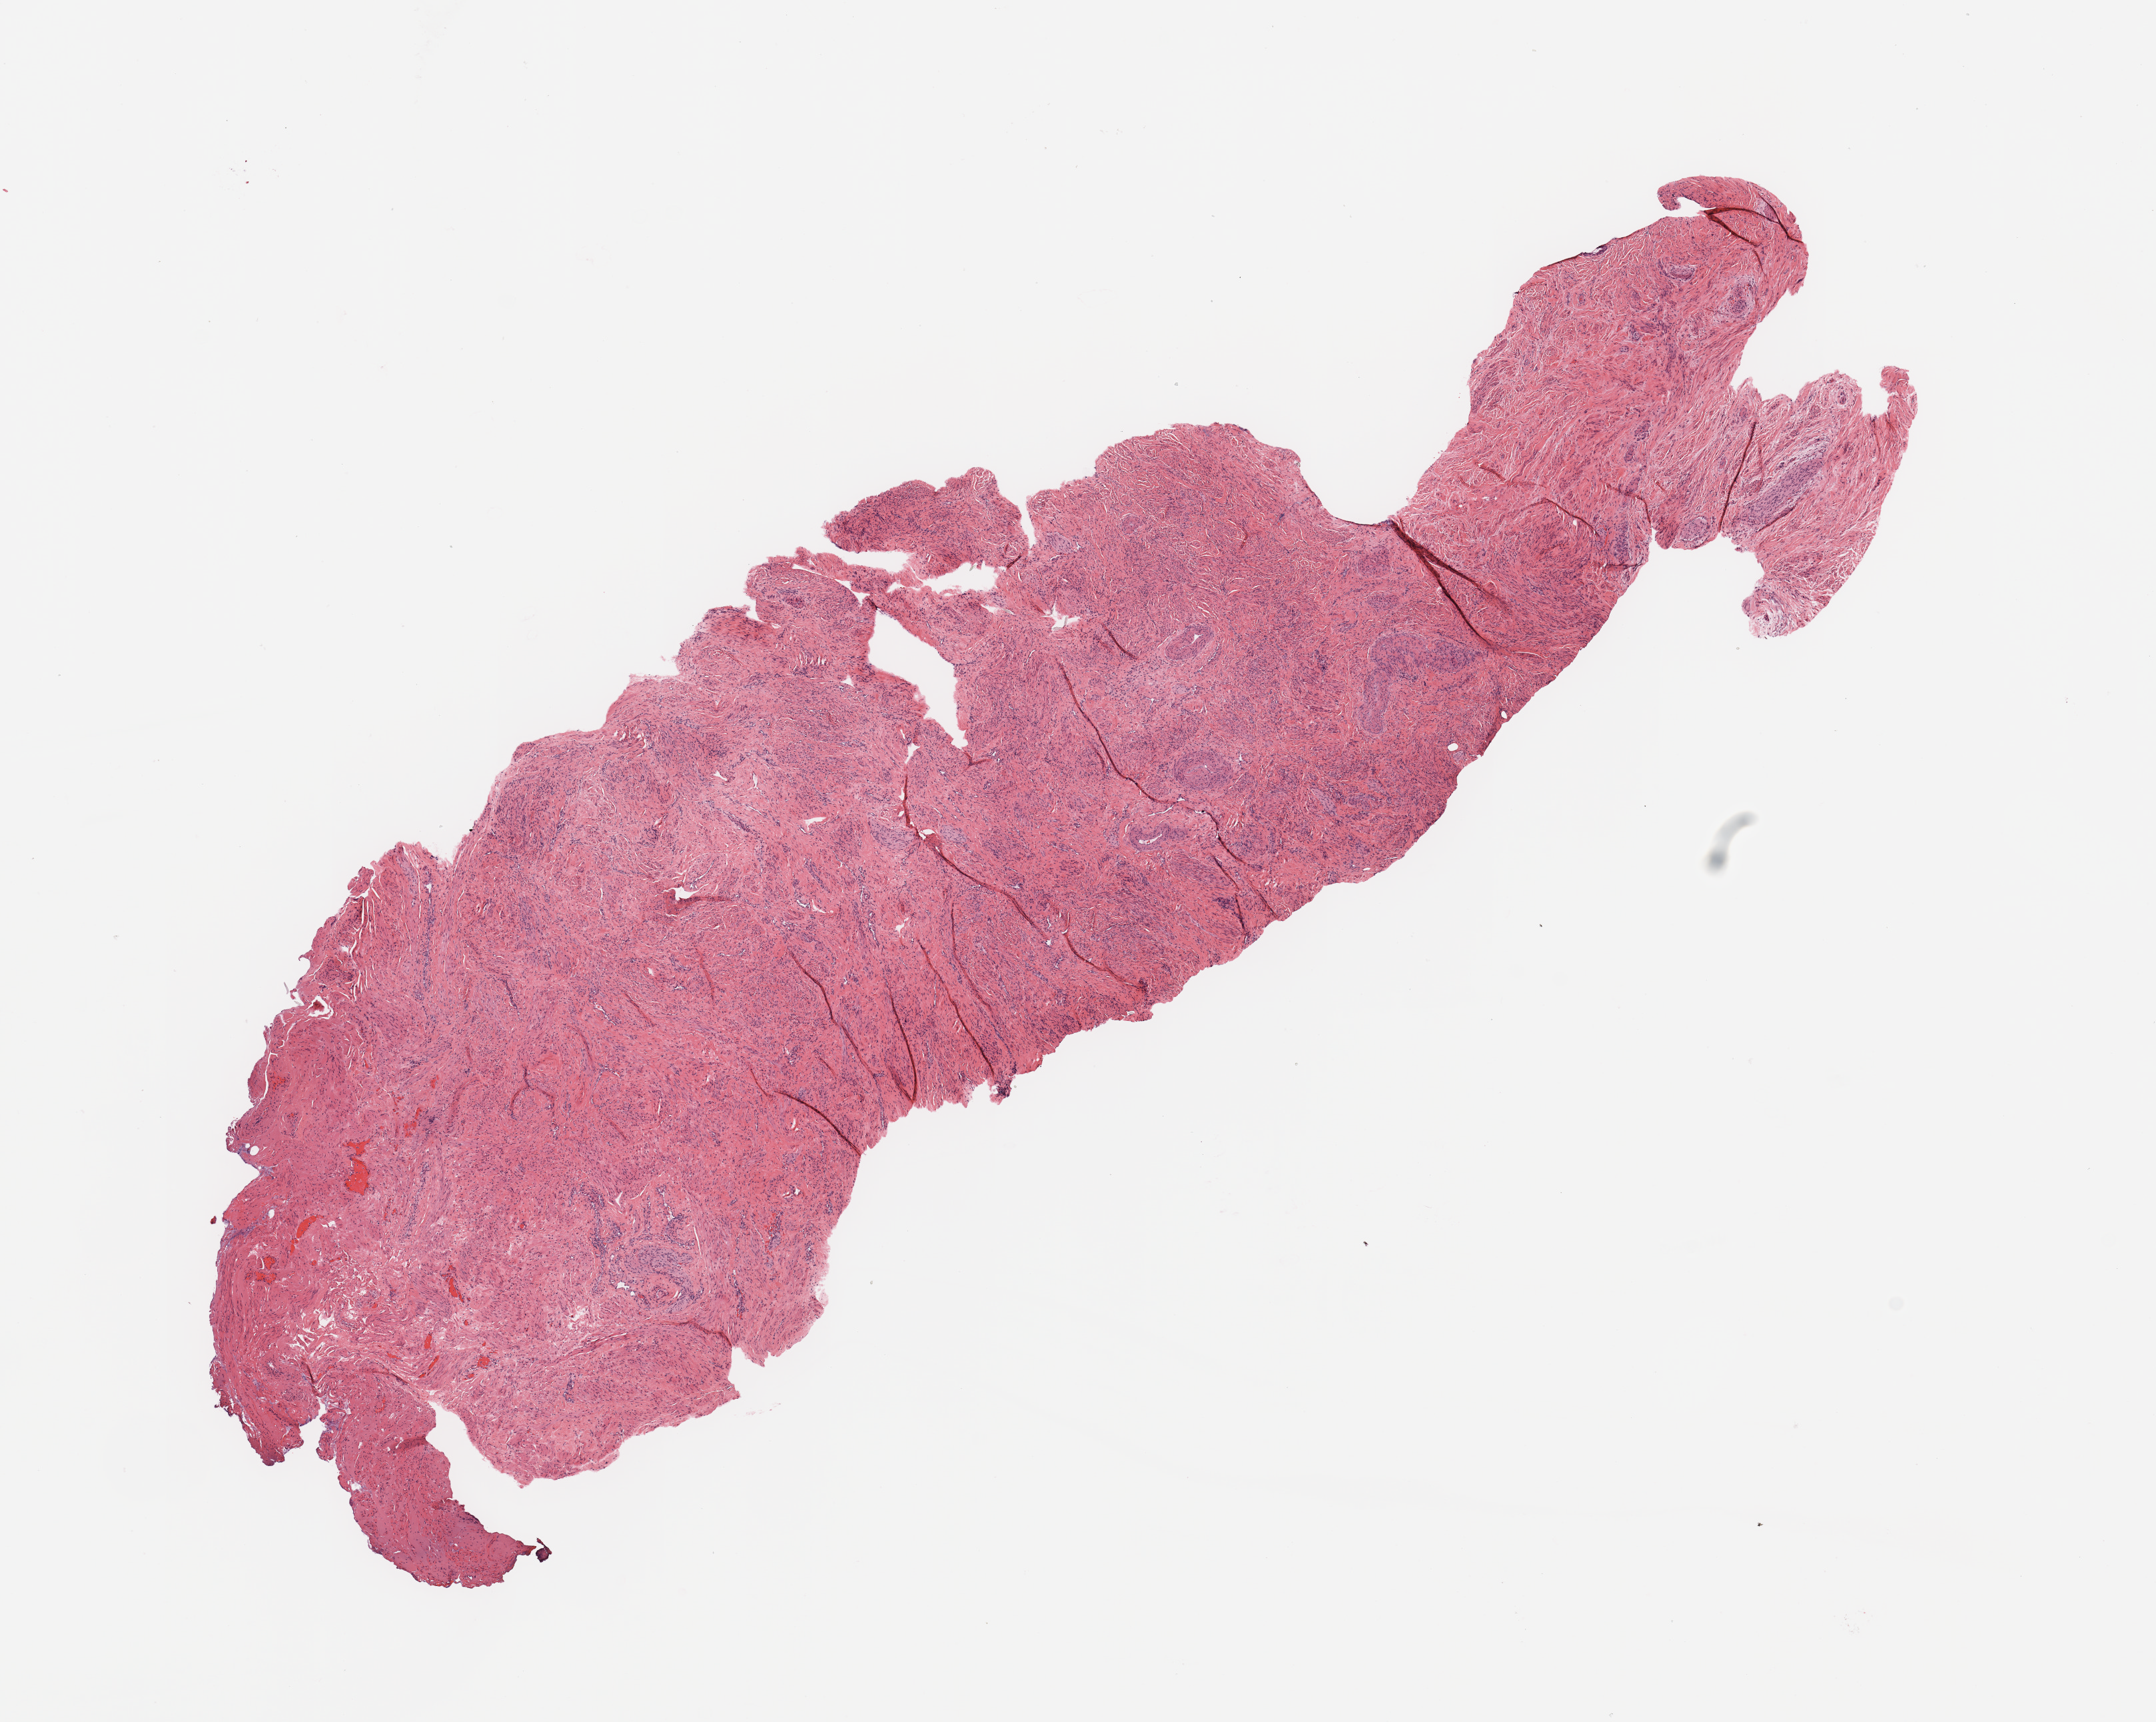
H&E whole-slide image — a low-resolution overview of the entire scanned area, about 12.8 x 10.2 mm (acquisition: 20x scan), uterus, normal (non-tumour) tissue. 67-year-old female patient.
* this section: normal (non-tumour) tissue from the same patient
* patient diagnosis: Endometrioid adenocarcinoma, NOS